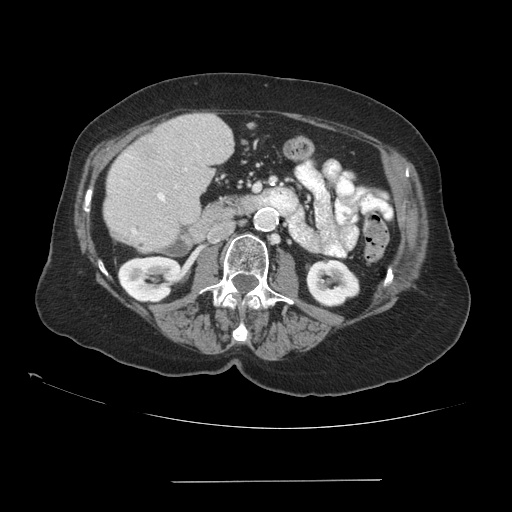
Contrast-enhanced abdominal CT (liver protocol), one axial slice; reconstruction kernel STANDARD; soft-tissue window (W 400 / L 40 HU); 2.5 mm slice thickness; 512 × 512 image matrix, field of view 400 × 400 mm. From the clinical record (not read from this slice): diagnosis: hepatocellular carcinoma (patient treated with transarterial chemoembolisation; whether this scan precedes or follows treatment is not stated here); TNM stage (as recorded): Stage-IVA.
Structures marked on this image (semi-automatically segmented with operator editing):
- liver parenchyma outside the tumour (the mass and vessels are separate outlines, so this box may not span the whole liver): bounding box [x1, y1, x2, y2] px = [104, 114, 234, 250]
- mass: [131, 136, 158, 160]
- liver vessels: [129, 156, 186, 234]